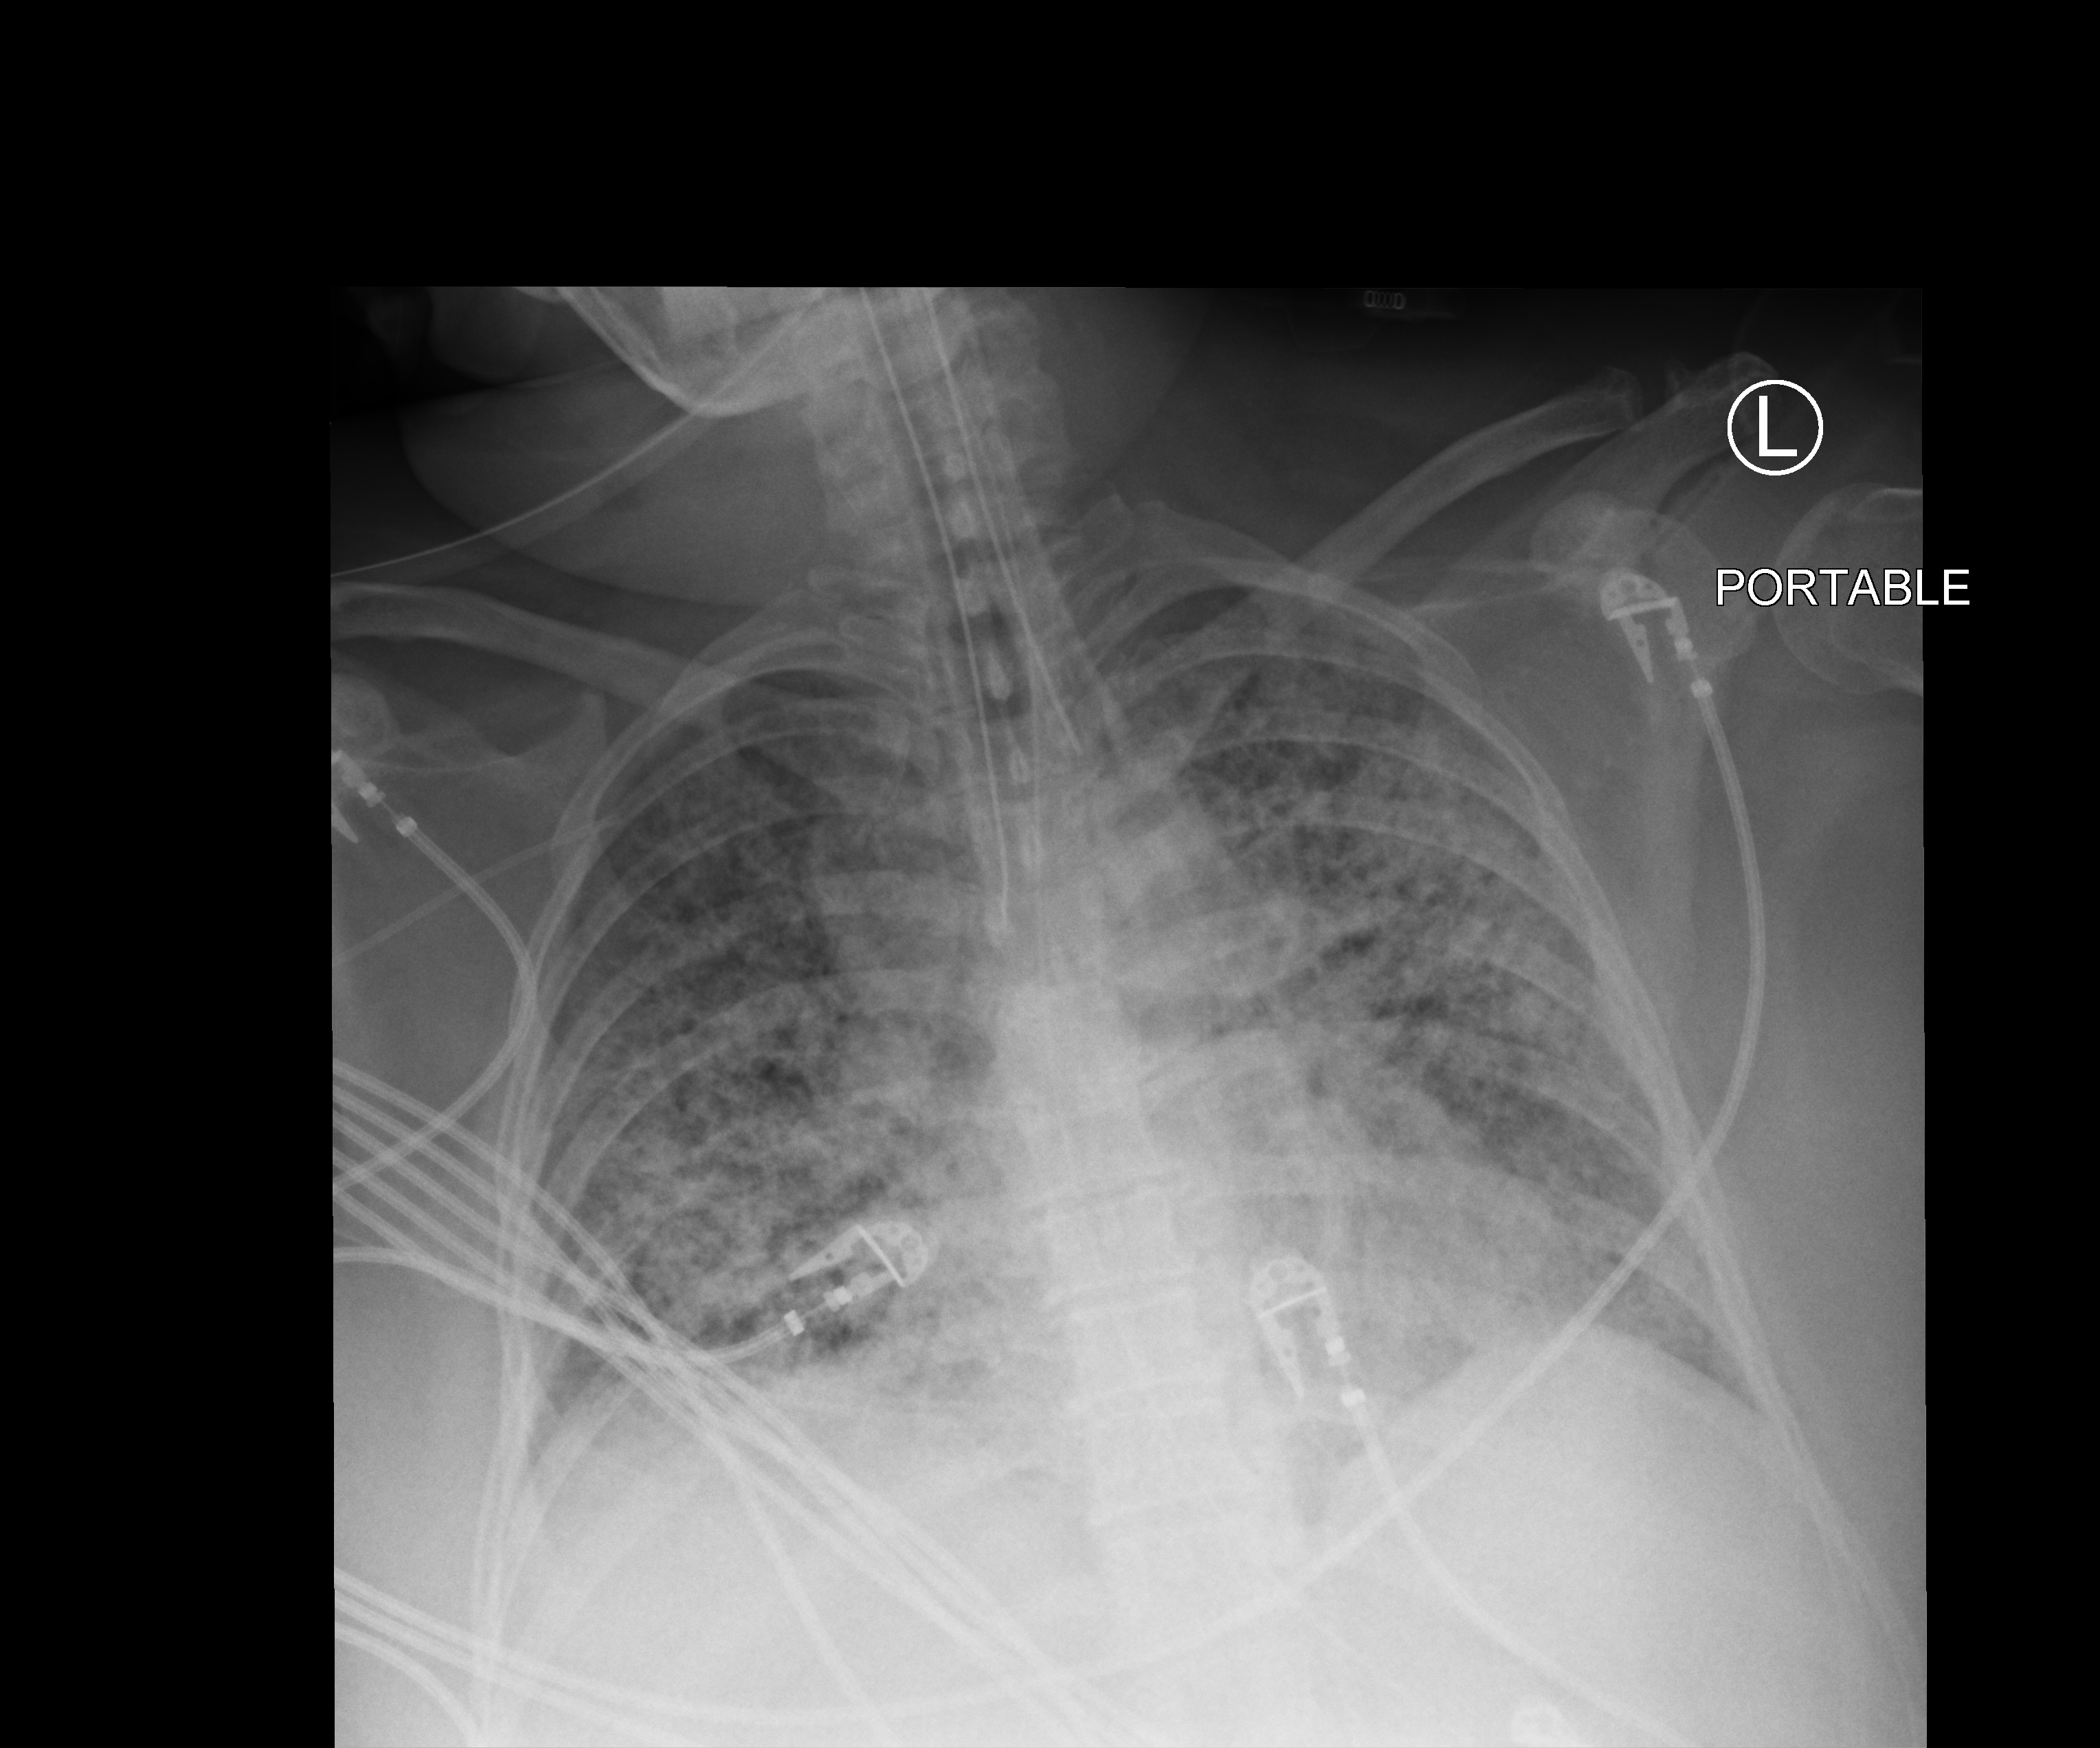
Chest X-ray (portable), anteroposterior (AP) projection. Female patient hospitalised with COVID-19, age 18–59 years.
Hospital-stay facts (about this admission, not read from this image; timing relative to this image not recorded):
- mechanically ventilated during this hospital stay: yes
- other chronic lung disease (admission record): no
- admitted to intensive care during this hospital stay: yes